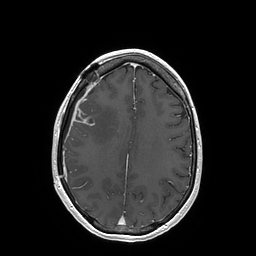
Brain MRI from a brain-tumour surgery series, one axial slice; slice 62 of 202 in the series (ordered by position); T1-weighted post-contrast; 256 × 256 image matrix, field of view 250 × 250 mm. Case-level facts recorded for this patient, not image findings: histopathology: Glioblastoma; WHO grade: 4; IDH mutation: no.
Annotated regions visible in this slice (manually delineated by an expert):
- tumour: bounding box <74,109,93,125> (left, top, right, bottom; pixels)